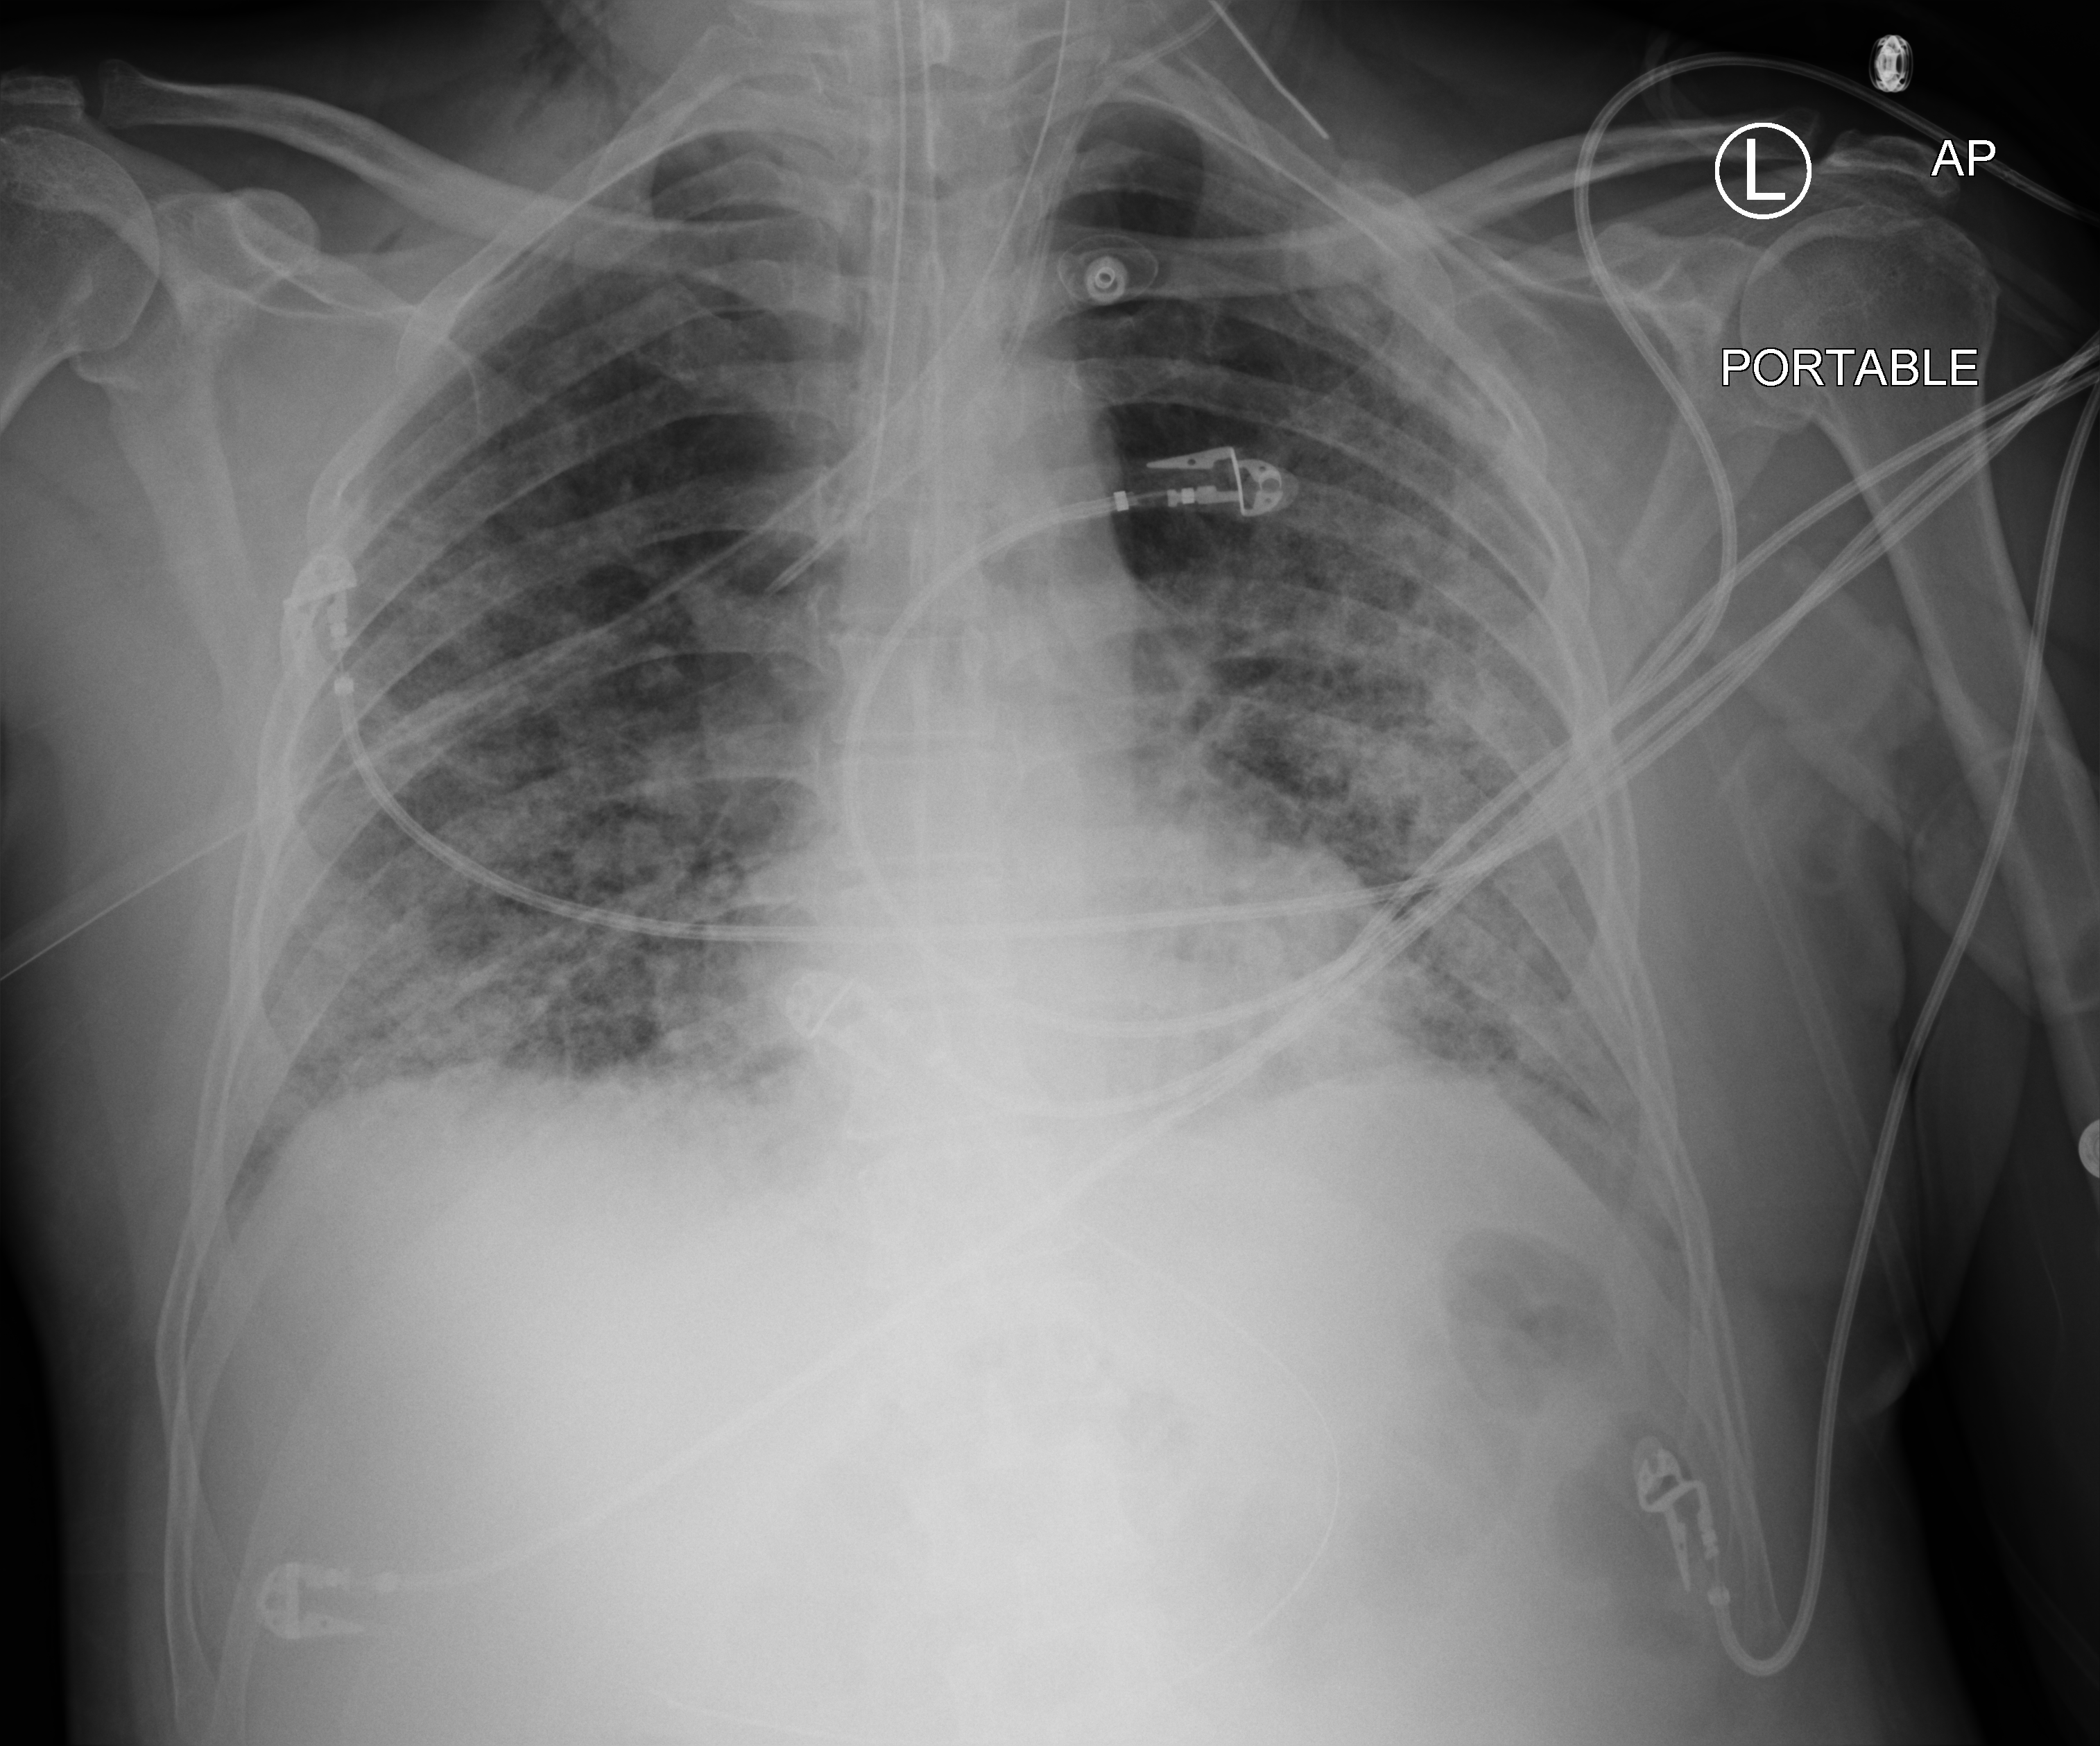
Portable chest radiograph; anteroposterior (AP) projection. Male patient hospitalised with COVID-19, age 60–74 years.
Admission-level facts for this patient (not findings on this image; timing relative to this image not recorded): diabetes (admission record): no; mechanically ventilated during this hospital stay: yes.